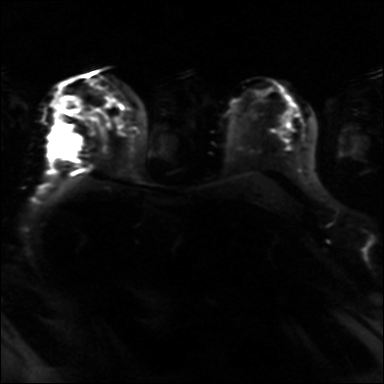
Breast MRI, one axial slice; position 21 of 36 along the scan axis; diffusion-weighted series; image 2 of 4 stored at this slice position (different b-values; order by instance number); 3 T; 4 mm slice thickness; 384 × 384 image matrix, field of view 320 × 320 mm. Female patient.
Annotated regions visible in this slice (expert manual segmentation):
- tumour on diffusion-weighted imaging: bounding box <55,133,81,158> (left, top, right, bottom; pixels)